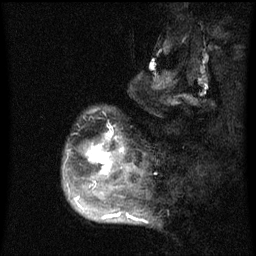
Breast MRI (dynamic contrast-enhanced), one sagittal slice; position 14 of 60 along the scan axis; dynamic contrast-enhanced series, image 2 of 3 at this slice position (ordered by acquisition); 1.5 T; TE 4.2 ms, TR 8 ms; 2 mm slice thickness; 256 × 256 image matrix, field of view 190 × 190 mm. Female patient, age 50 years.
Annotated regions visible in this slice (semi-automatically segmented with operator editing):
- analysis volume of interest (the breast-tissue region the enhancement analysis was run in; not a lesion): bounding box <62,107,142,216> (left, top, right, bottom; pixels)
- tumour enhancement mask (voxels above the 70 % enhancement threshold inside the analysis volume of interest): <67,132,131,216>